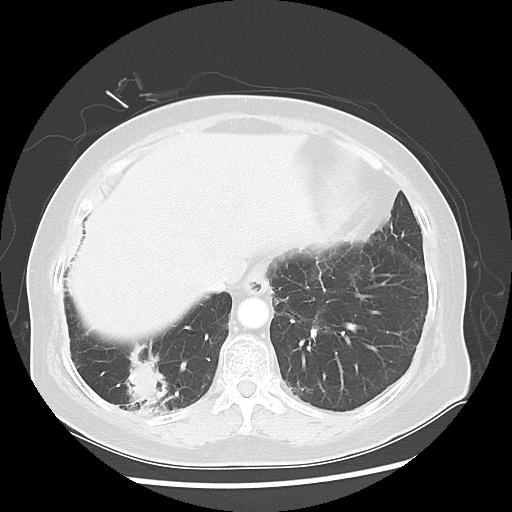
Chest CT, one axial slice; slice 14 of 56 in the series (ordered by position); reconstruction kernel LUNG; lung window (W 1500 / L -600 HU); 5 mm slice thickness; 512 × 512 image matrix, field of view 360 × 360 mm. Female patient, age 64 years. Case-level facts recorded for this patient, not image findings: clinical TNM (as recorded): Tis N0 M0.
Structures marked on this image (rectangle marked by the reading radiologist):
- lung tumour (recorded histology: adenocarcinoma): box from (x=110, y=330) to (x=181, y=427) px